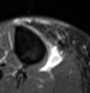
MRI of an extremity soft-tissue mass, one axial slice. Slice 36 of 60 in the series (ordered by position). STIR. MR volume resampled by the dataset authors to the PET/CT grid (not the native acquisition matrix). 90 × 93 image matrix, field of view 88 × 91 mm. Female patient. Case-level facts recorded for this patient, not image findings: histological type: undifferentiated – high grade; grade: high; site of the primary tumour: right thigh.
Annotated regions visible in this slice (expert contour drawn on MRI and transferred to this co-registered scan by the dataset authors):
- gross tumour volume (mass): bounding box (x1, y1, x2, y2) in pixels: (46, 46, 63, 70)